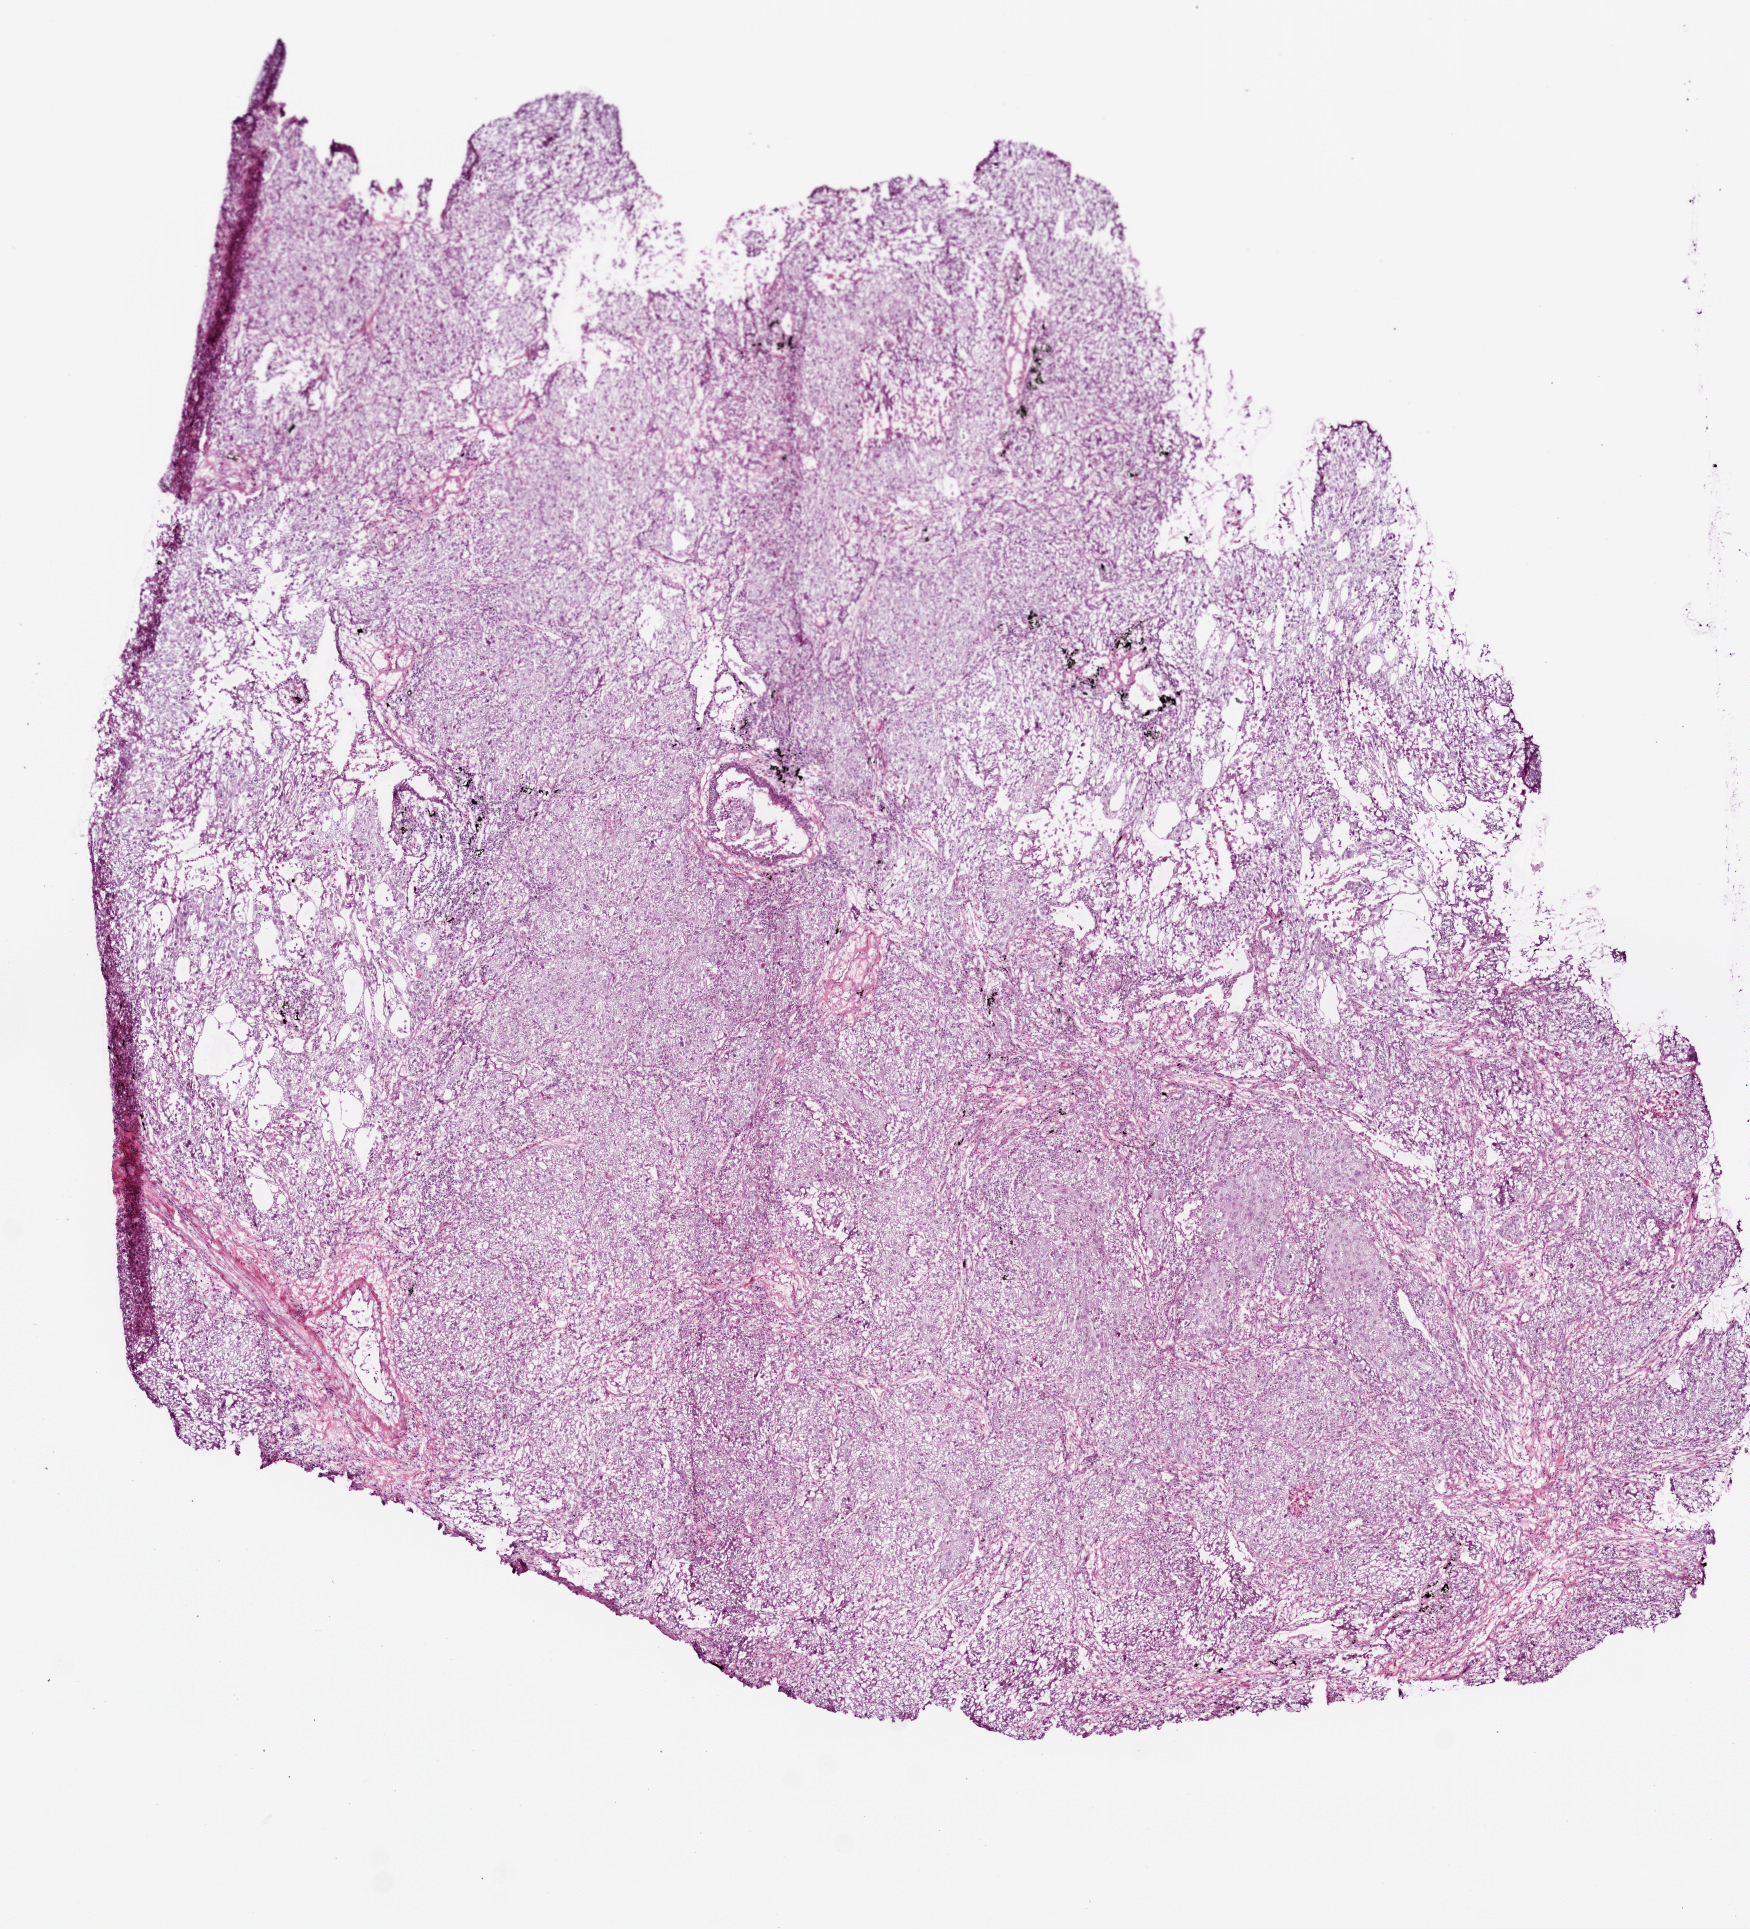
Whole-slide histology image, H&E, a low-resolution overview of the entire scanned area, about 7.0 x 7.7 mm. Frozen section from the top of the tissue portion. Primary tumour sample from the lung. Male patient. Composition of this section per pathologist review: tumour cells 90%, tumour nuclei 80%, normal cells 0%, stromal cells 5%, necrosis 5%.
Pathologic diagnosis: Adenocarcinoma, NOS (upper lobe, lung). Laterality: right. AJCC pathologic stage: IIB (6th edition).